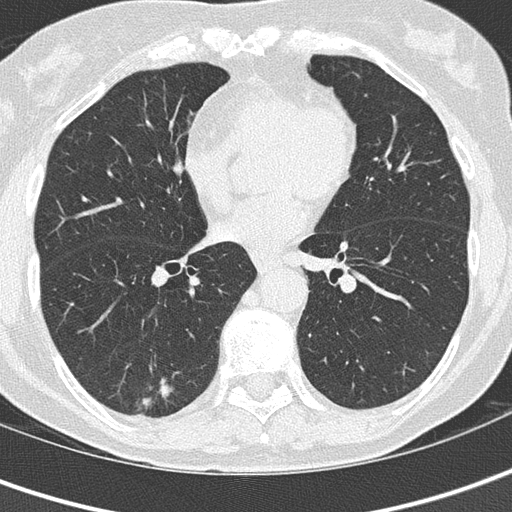
Axial slice from a low-dose chest CT screening exam; second screening round (one year after baseline); lung window (W 1500 / L -600 HU); 2 mm slice thickness; 120 kVp; slice 87 of 152 in the series. Female participant, aged 69 years at enrolment. Current smoker at enrolment.
Expert reader's lesion annotation, bounding box (x1, y1, x2, y2) in pixels: (120, 362, 182, 425). The screening reader recorded 2 non-calcified nodules or masses ≥4 mm on this exam (right lower lobe, left lower lobe); which of them this box marks is not recorded. Official screen result: positive, other. Participant outcome: lung cancer diagnosed 112 days after this screen — adenocarcinoma, NOS, right lower lobe, moderately differentiated (G2), stage IA (AJCC 6th edition), 16 mm at pathology.